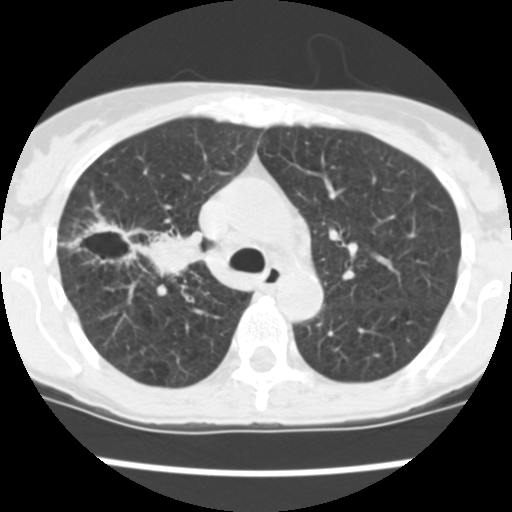
Chest CT (low-dose screening protocol), one axial image, first (baseline) screen, lung window (W 1500 / L -600 HU), 2.5 mm slice thickness, slice 168 of 252 in the series, 512 × 512 image matrix, field of view 276 × 276 mm. Female, age 60 years at enrolment. Current smoker at enrolment.
Lesion marked by an expert reader, bounding box (x1, y1, x2, y2) in pixels: (83, 216, 194, 284). The screening reader recorded 3 non-calcified nodules or masses ≥4 mm on this exam (right upper lobe, right upper lobe, right lower lobe); which of them this box marks is not recorded. Official screen result: positive, change unspecified: nodule(s) >= 4 mm or enlarging nodule(s), mass(es), or other non-specific abnormalities suspicious for lung cancer. Participant outcome: lung cancer diagnosed 19 days after this screen — non-small cell carcinoma, right upper lobe, stage IV (AJCC 6th edition), 26 mm at pathology.